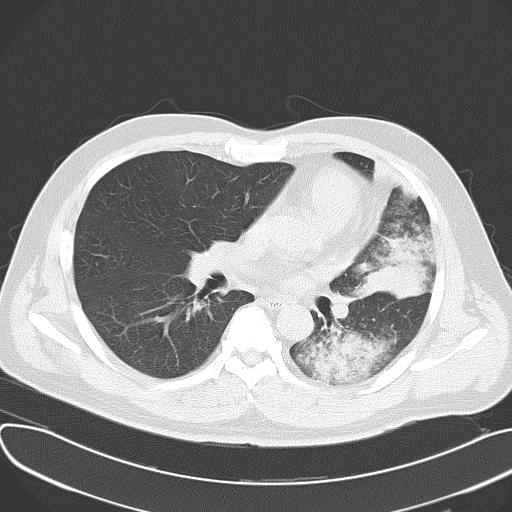
Chest CT, one axial slice; slice 34 of 62 in the series (ordered by position); reconstruction kernel B70f; lung window (W 1500 / L -600 HU); 5 mm slice thickness; 512 × 512 image matrix. Patient: male, 48 years. Case-level facts recorded for this patient, not image findings: clinical TNM (as recorded): T4 N0 M0.
Annotated regions visible in this slice (bounding box drawn by a radiologist):
- lung tumour (recorded histology: adenocarcinoma): bounding box <361,233,431,306> (left, top, right, bottom; pixels)